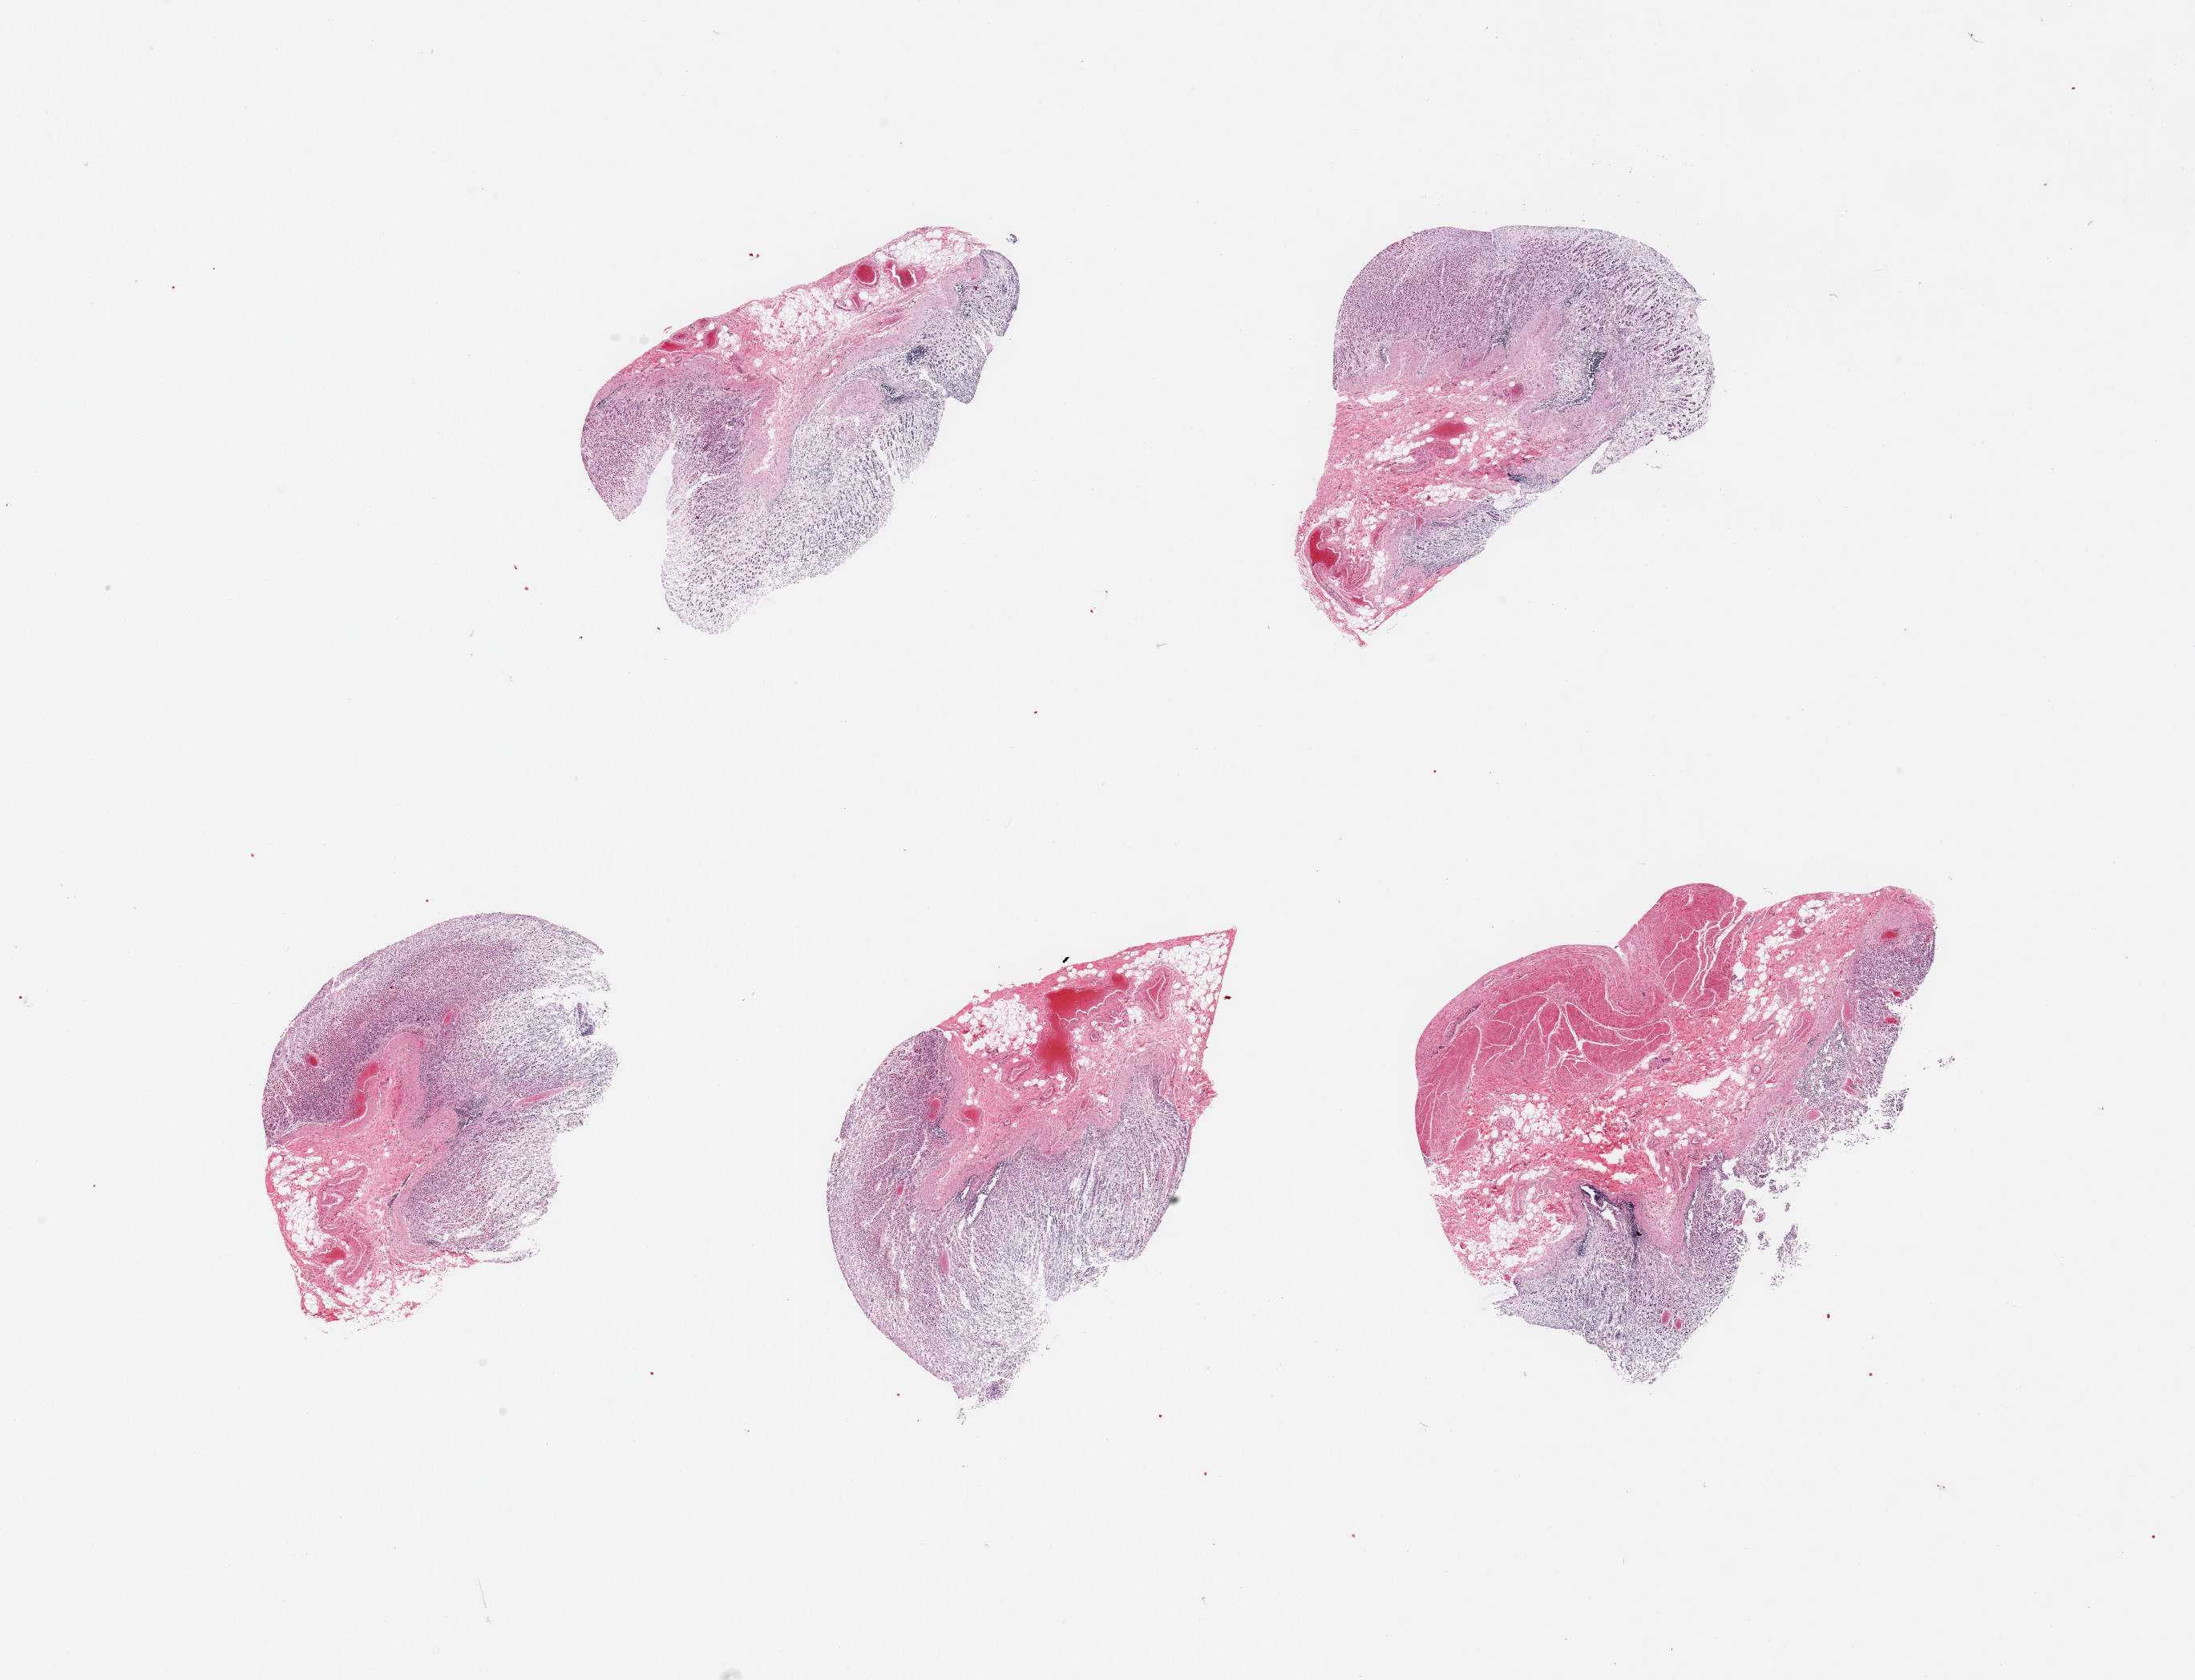
Whole-slide image, hematoxylin and eosin (H&E) stain, brightfield — shown as a low-resolution overview of the whole scanned area (about 21.7 x 16.6 mm). PAXgene-fixed, paraffin-embedded tissue. Sampled site (target tissue): gastroesophageal junction. Donor tissue sample. Donor: male.
Review note (as recorded): 5 pieces; autolyzed gastric mucosa is main component.